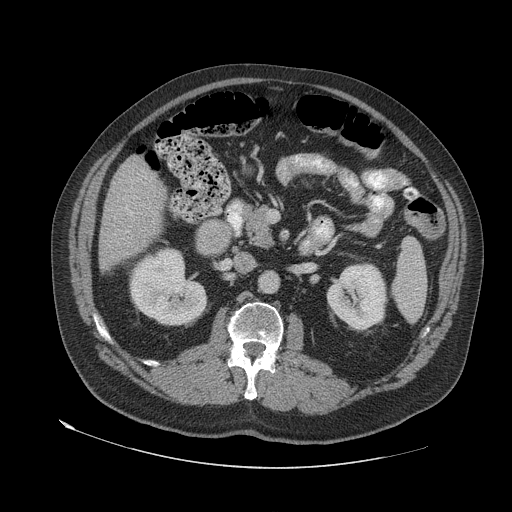
Contrast-enhanced abdominal CT (liver protocol), one axial slice. Slice 20 of 79 in the series (ordered by position). 140 kVp. Soft-tissue window (W 400 / L 40 HU). 2.5 mm slice thickness. 512 × 512 image matrix, field of view 480 × 480 mm. Case-level facts recorded for this patient, not image findings: diagnosis: hepatocellular carcinoma (patient treated with transarterial chemoembolisation; whether this scan precedes or follows treatment is not stated here); TNM stage (as recorded): Stage-IVA.
Outlined on this slice (semi-automatically segmented with operator editing):
- liver parenchyma outside the tumour (the mass and vessels are separate outlines, so this box may not span the whole liver): bounding box [x1, y1, x2, y2] px = [98, 156, 166, 271]
- liver vessels: [131, 212, 133, 214]